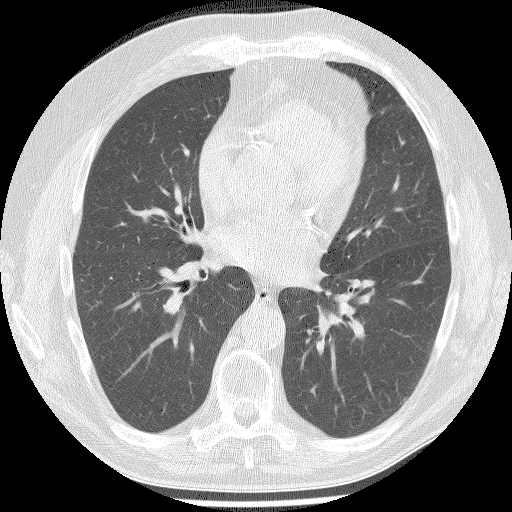
Axial slice from a low-dose chest CT screening exam. Second screening round (one year after baseline). Lung window (W 1500 / L -600 HU). 2.5 mm slice thickness. Lung (sharp) reconstruction kernel (BONE). Male participant, aged 61 years at enrolment.
Expert reader's lesion annotation, bounding box (x1, y1, x2, y2) in pixels: (119, 195, 159, 239). The screening reader recorded 2 non-calcified nodules or masses ≥4 mm on this exam (right upper lobe, right lower lobe); which of them this box marks is not recorded. Official screen result: positive, other. Participant outcome: lung cancer diagnosed 147 days after this screen — bronchiolo-alveolar adenocarcinoma, NOS, right middle lobe, well differentiated (G1), stage IA (AJCC 6th edition), 15 mm at pathology.